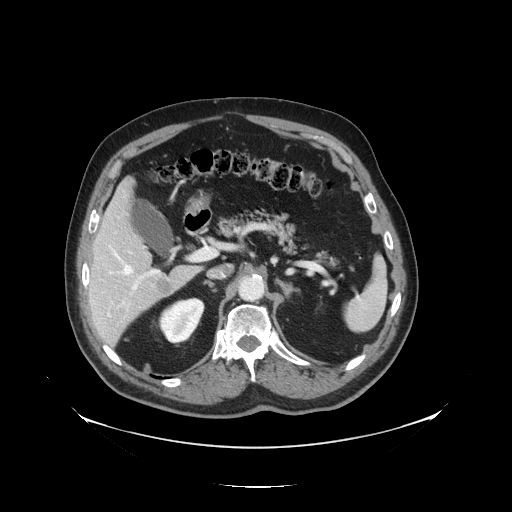
Contrast-enhanced abdominal CT, one axial slice; position 80 of 138 along the scan axis; 120 kVp; intravenous contrast given; soft-tissue window (W 400 / L 40 HU); 2.5 mm slice thickness; 512 × 512 image matrix. Male patient, age 77 years. Case-level facts recorded for this patient, not image findings: diagnosis: colorectal cancer liver metastases, imaged before liver resection; multiple liver metastases: no; largest metastasis: 1.5 cm; chemotherapy before resection: no.
Annotated regions visible in this slice (expert manual segmentation):
- hepatic veins: bounding box (x1, y1, x2, y2) in pixels: (112, 249, 133, 275)
- liver: (89, 182, 199, 345)
- planned liver remnant (the part of the liver to remain after resection): (88, 182, 155, 288)
- portal vein (with intrahepatic branches): (121, 253, 205, 308)
- liver metastasis: (157, 279, 173, 295)